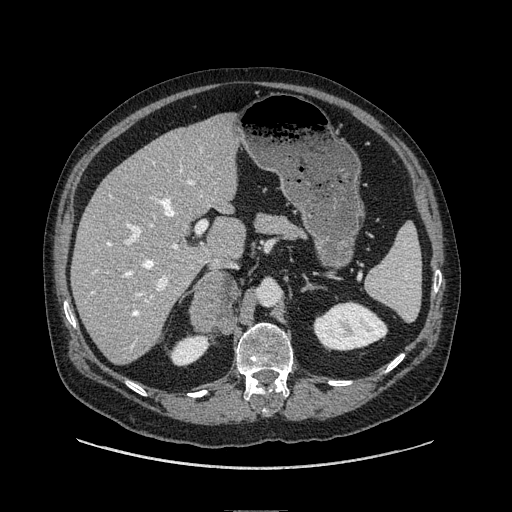
Contrast-enhanced abdominal CT, one axial slice; position 53 of 149 along the scan axis; soft-tissue window (W 400 / L 40 HU); 1.25 mm slice thickness; 512 × 512 image matrix. Male patient. Case-level facts recorded for this patient, not image findings: diagnosis: adrenocortical carcinoma; tumour side: right adrenal; tumour size at pathology: 7.5 cm; Ki-67 index: 15 %; stage (as recorded): 2.
Structures marked on this image (semi-automatic segmentation, software-assisted and operator-edited):
- mass: bounding box <191,272,239,332> (left, top, right, bottom; pixels)